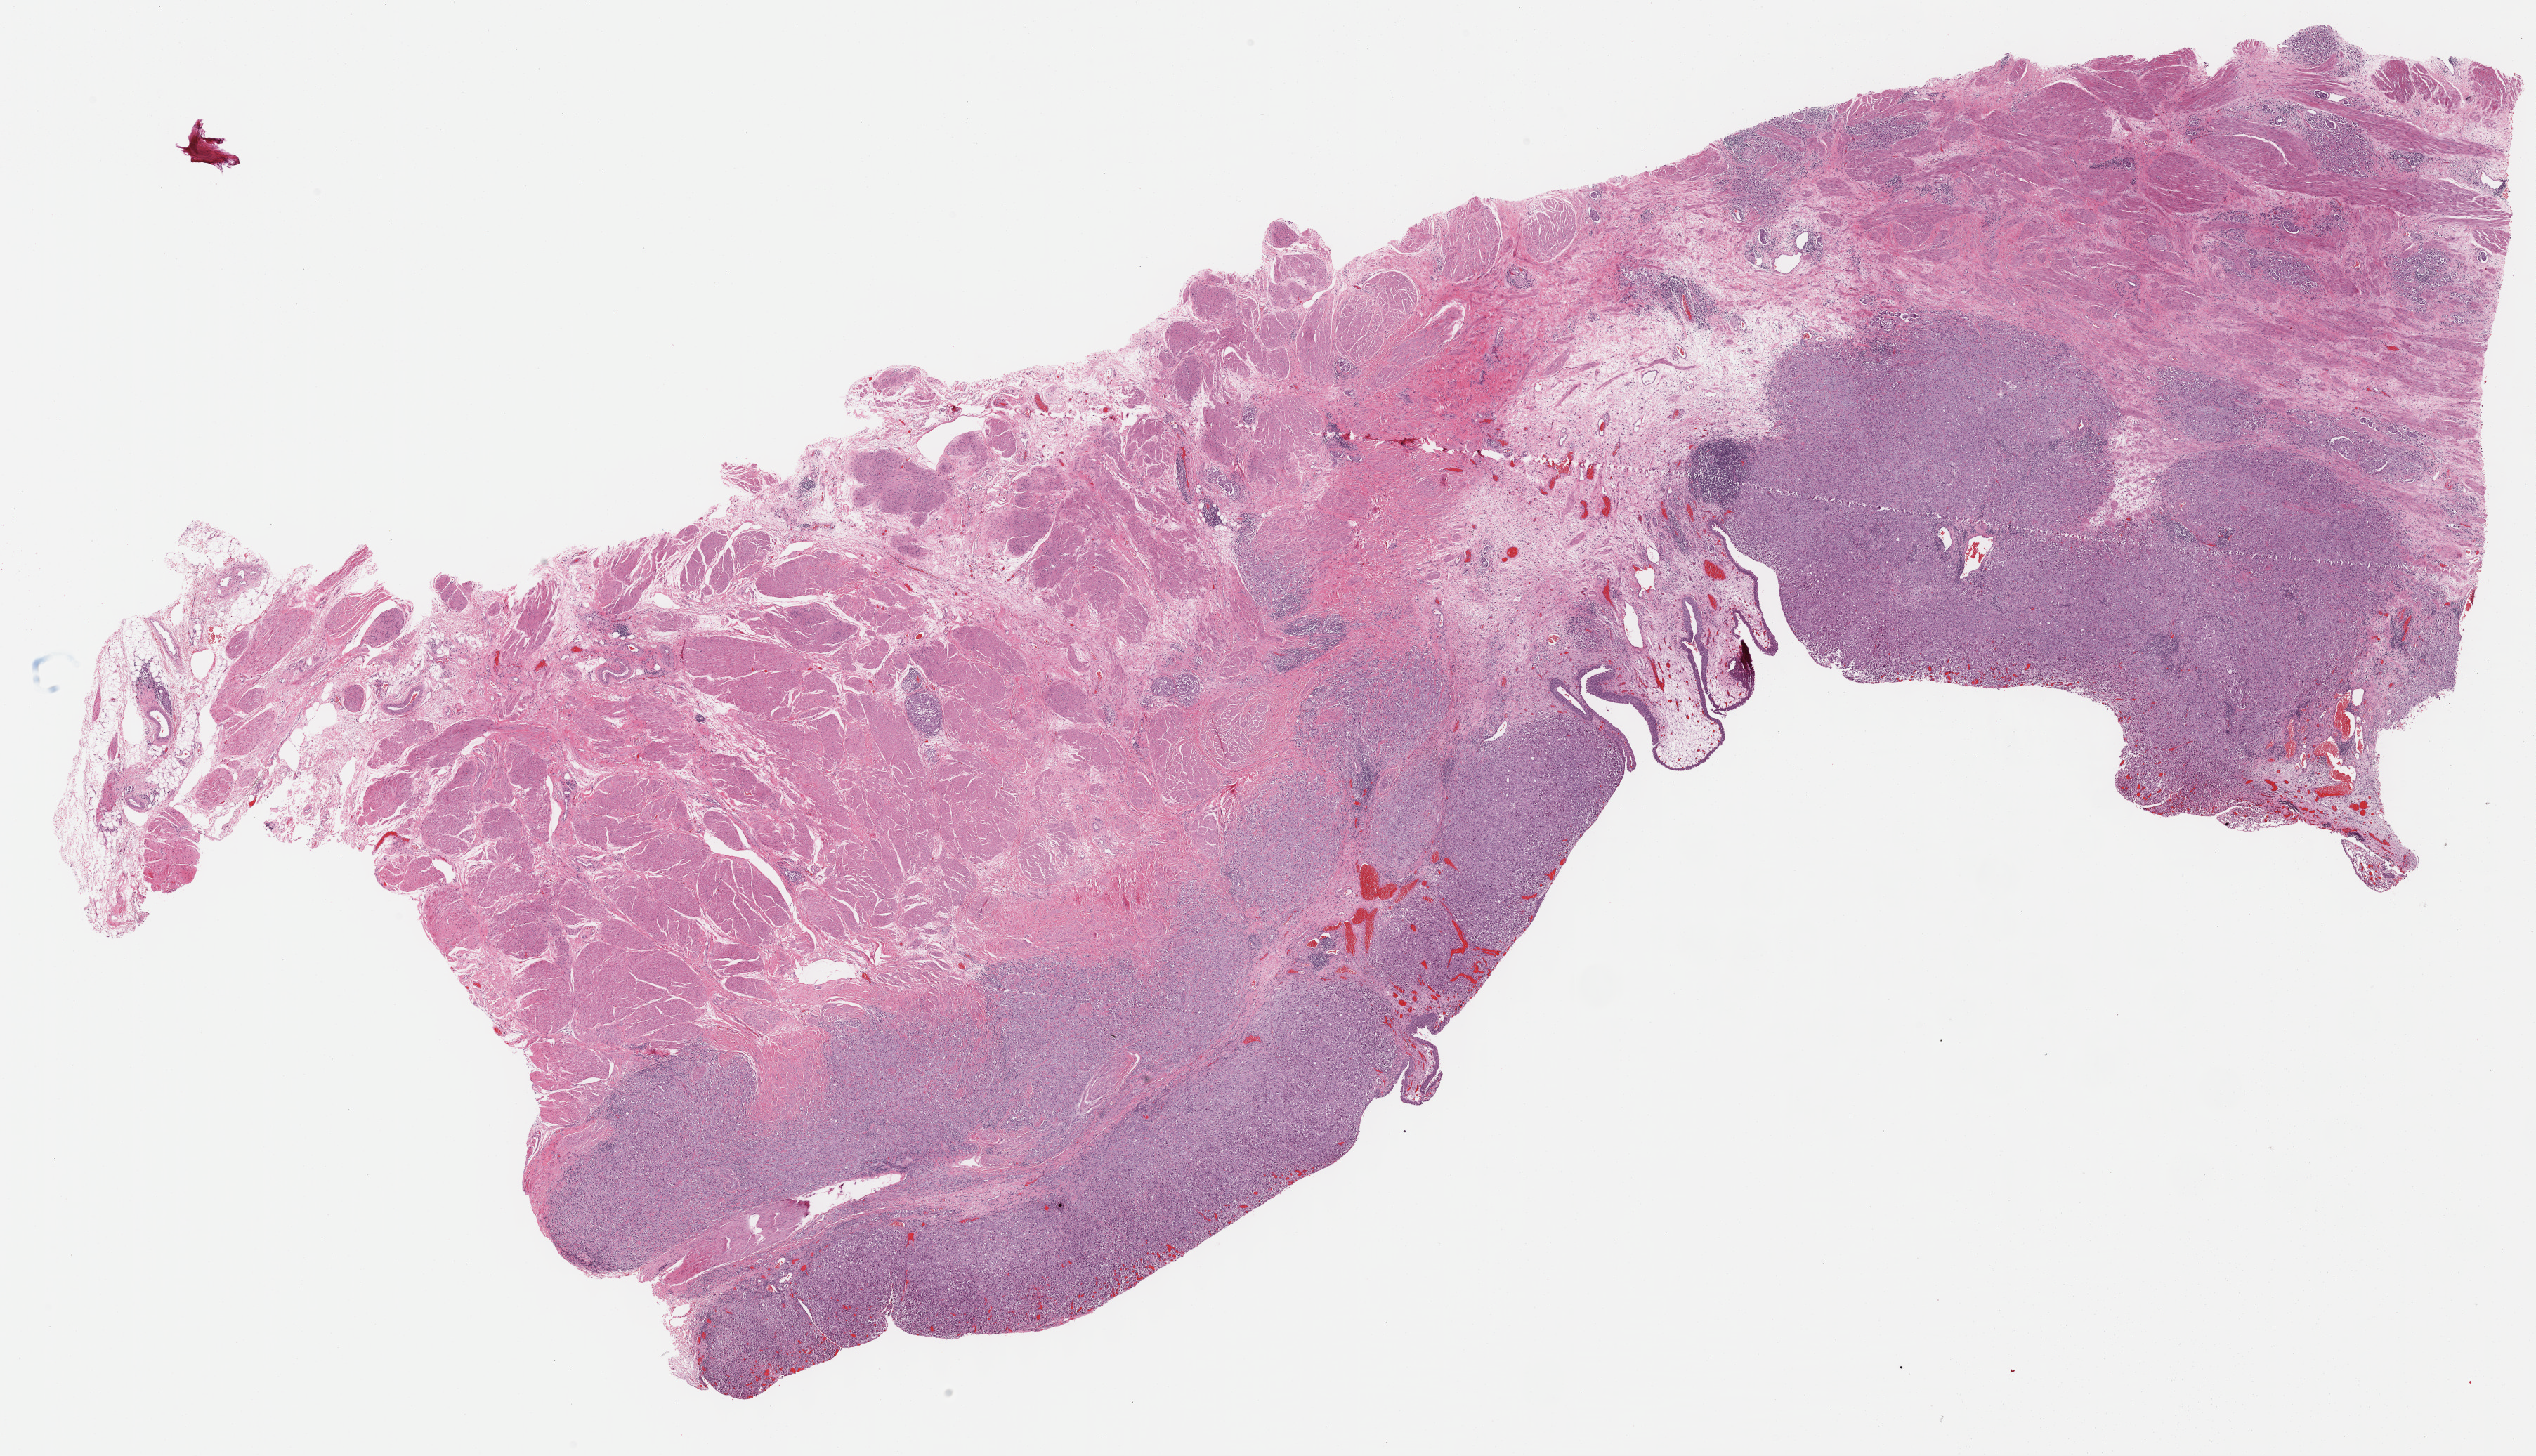
H&E-stained whole-slide image, a low-resolution overview of the entire scanned area, about 29.2 x 16.8 mm. Formalin-fixed paraffin-embedded (FFPE) diagnostic section. Primary tumour sample from the bladder. Male, age 60 years at initial diagnosis. Histologic grade: high grade.
AJCC pathologic stage: IV (6th edition). Pathologic diagnosis: Transitional cell carcinoma. Lymph nodes positive (case pathology): 12 of 18 examined.